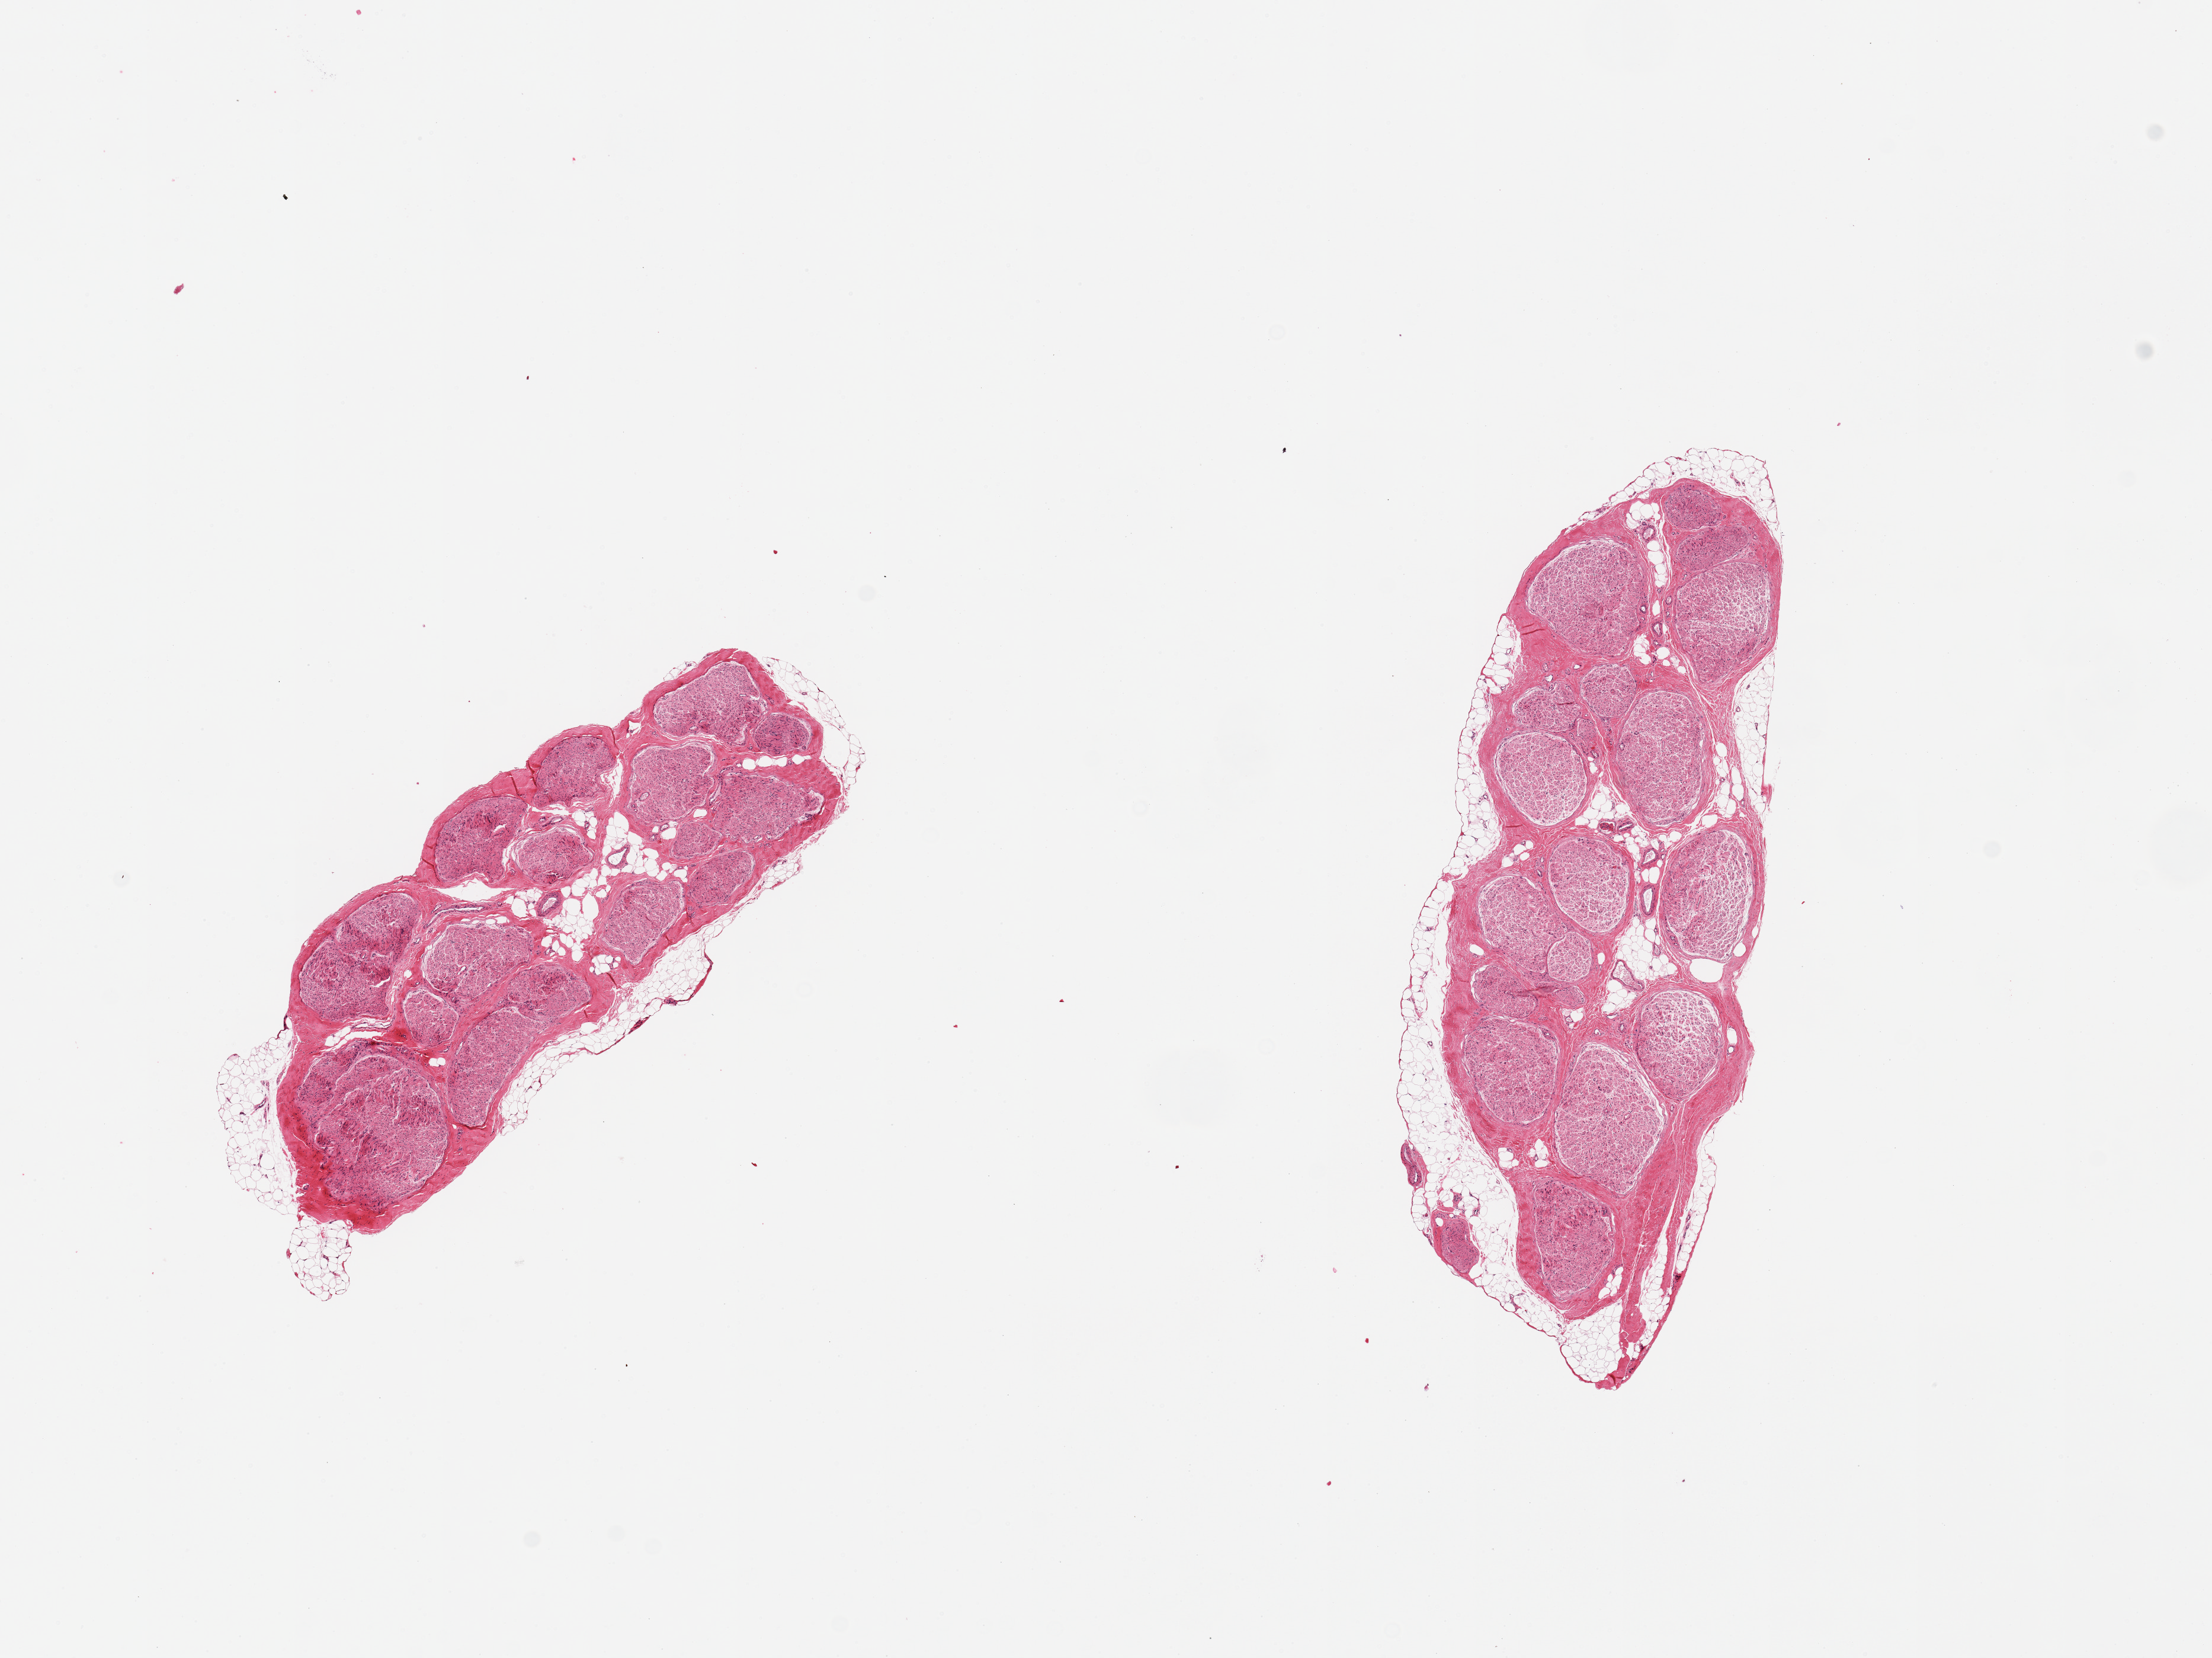
Haematoxylin and eosin whole-slide image — whole scanned area (about 14.8 x 11.1 mm) shown as a low-resolution overview. PAXgene-fixed paraffin-embedded (PFPE) section. Section of tibial nerve (target tissue). Tissue donor sample. Donor sex: male.
- reviewer comment on this tissue sample: 2 pieces; 10% external fat, 5% internal fat